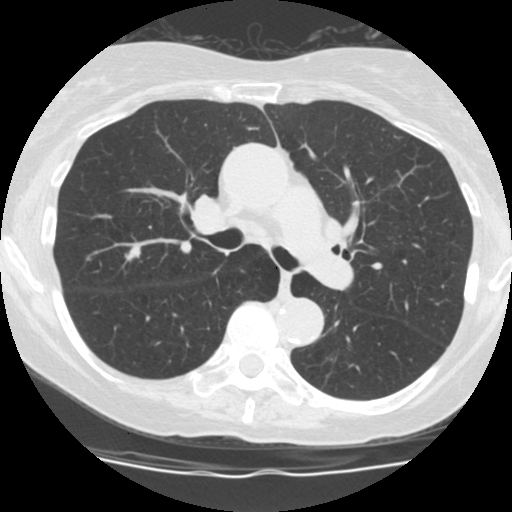
Low-dose screening chest CT, one axial slice; position 115 of 183 along the scan axis; reconstruction kernel STANDARD; lung window (W 1500 / L -600 HU); 512 × 512 image matrix, field of view 300 × 300 mm.
Annotated regions visible in this slice (expert manual segmentation):
- lesion 1 (tumor, upper lobe of right lung): bounding box (x1, y1, x2, y2) in pixels: (125, 245, 141, 261)